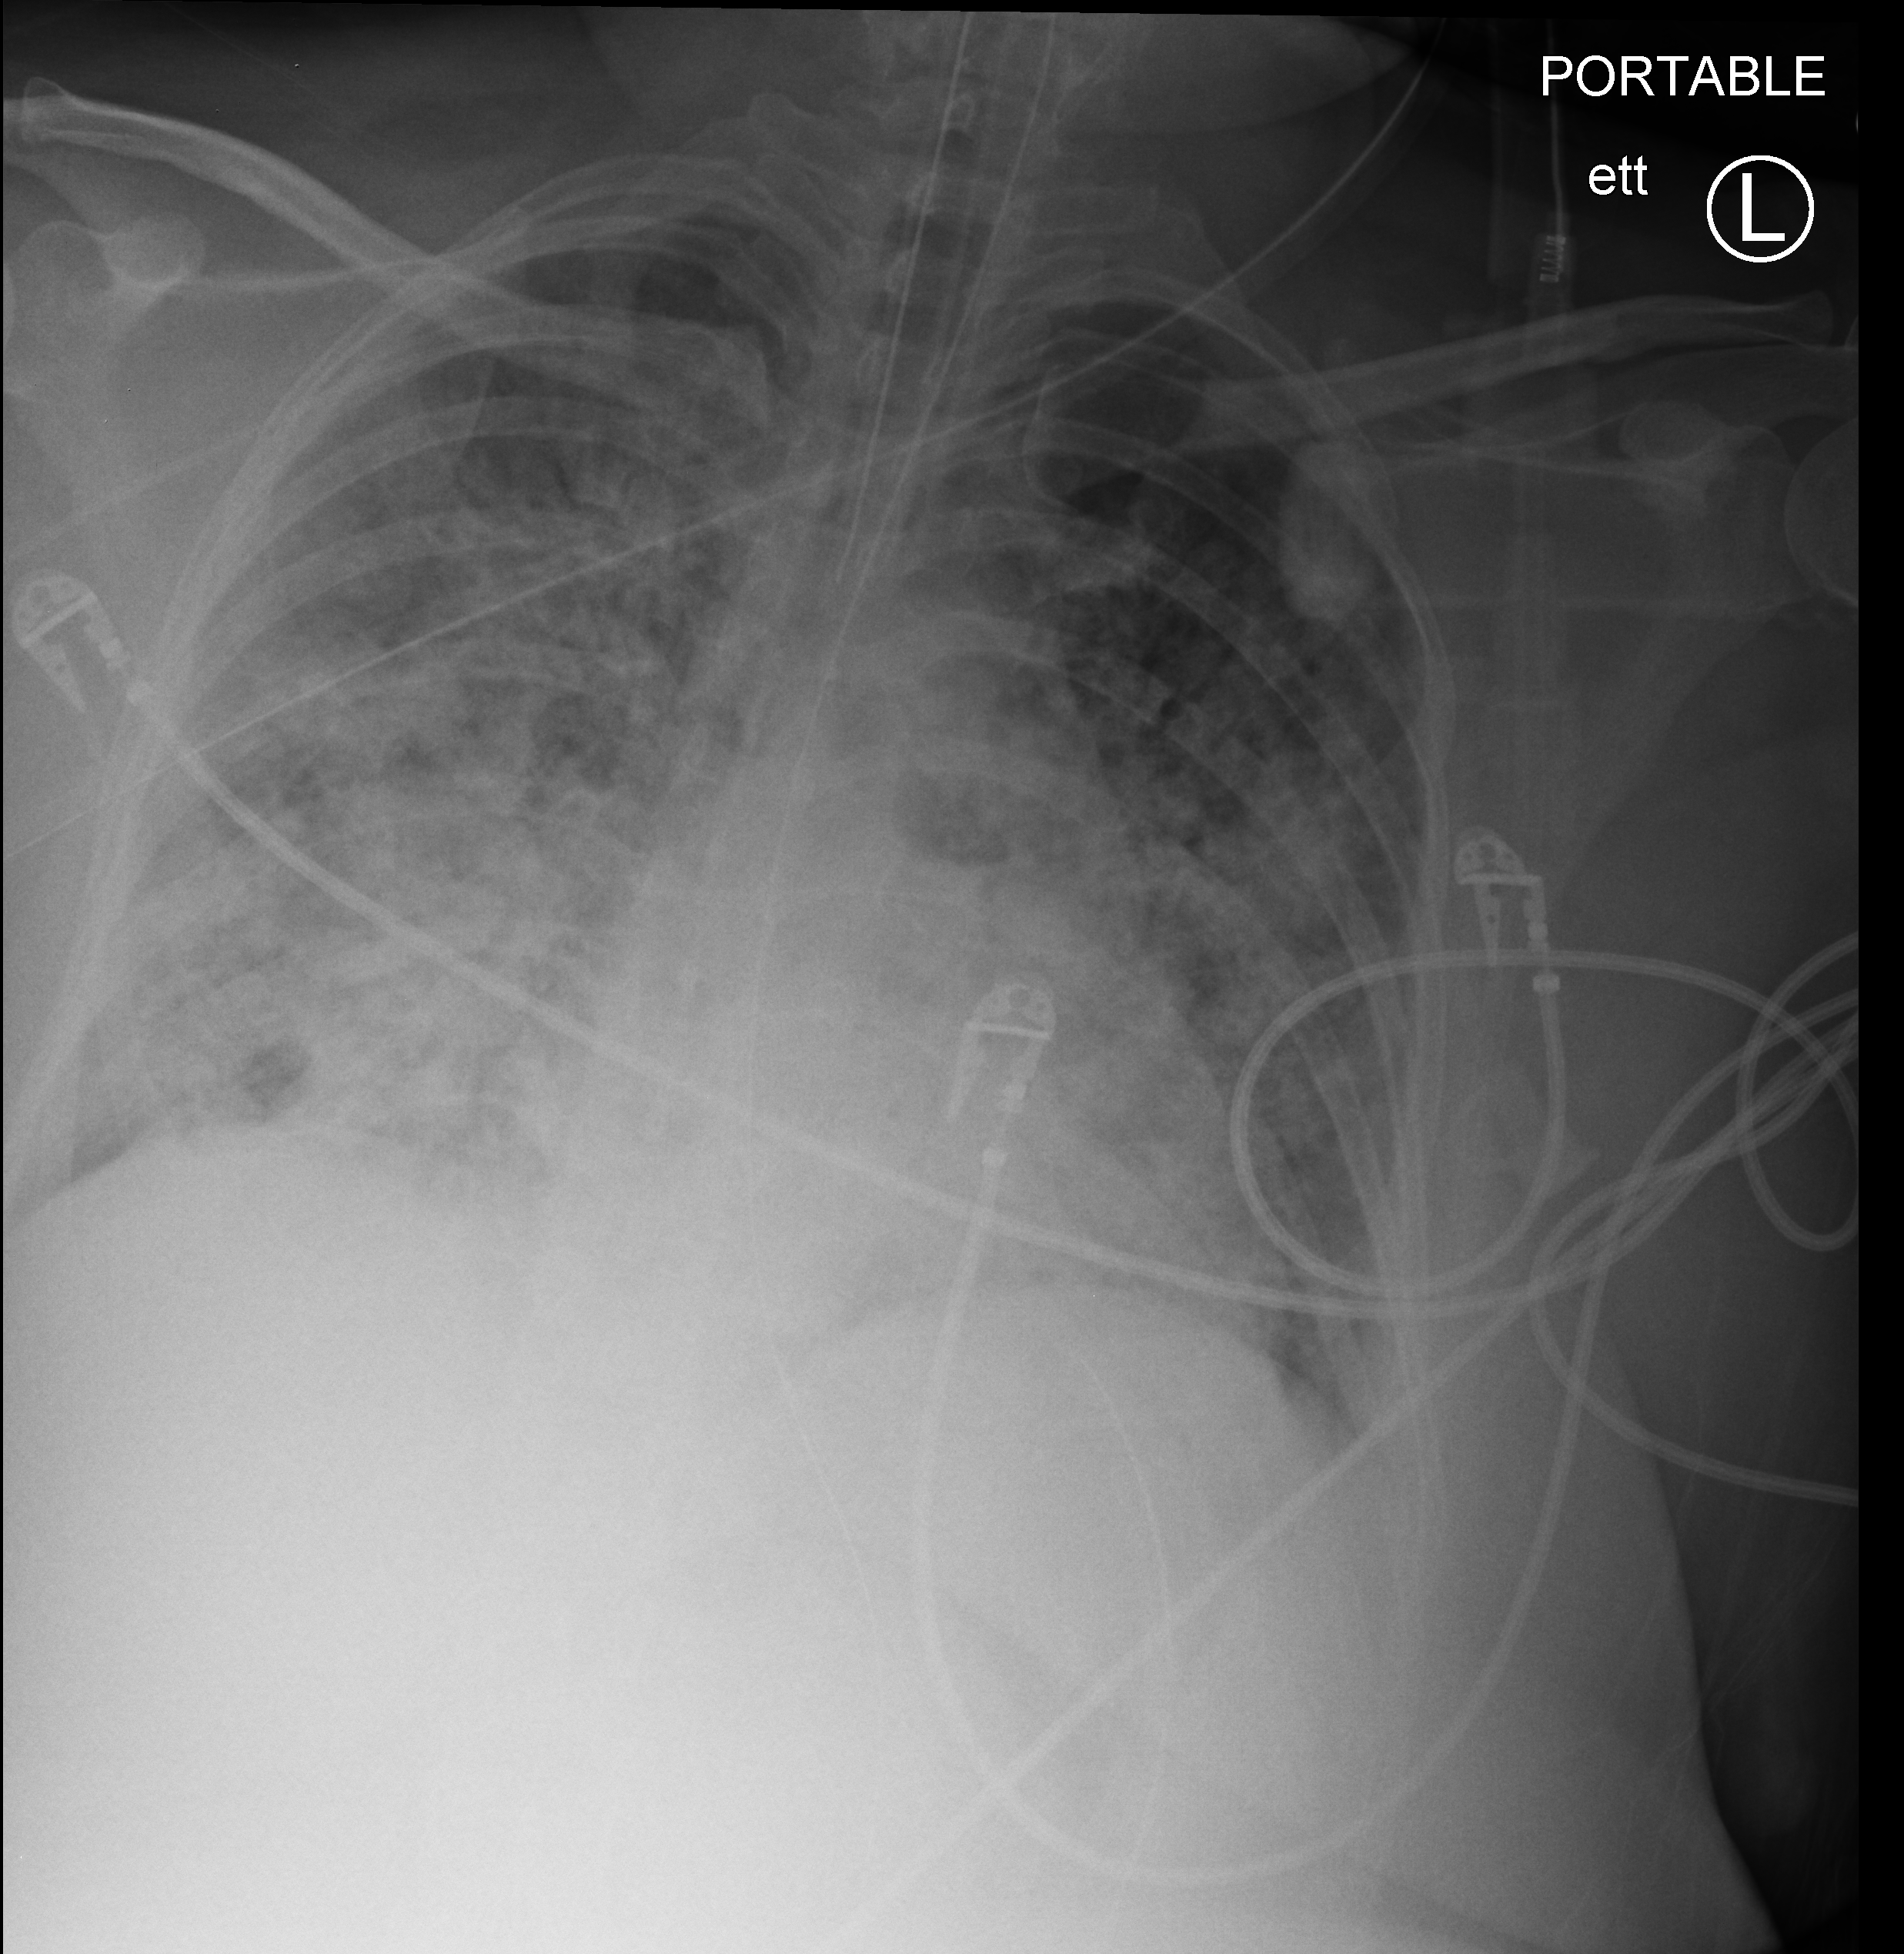
Bedside chest radiograph (computed radiography), anteroposterior (AP) projection. Patient hospitalised with COVID-19, aged 18–59 years.
Hospital-stay facts (about this admission, not read from this image; timing relative to this image not recorded): admitted to intensive care during this hospital stay: yes.